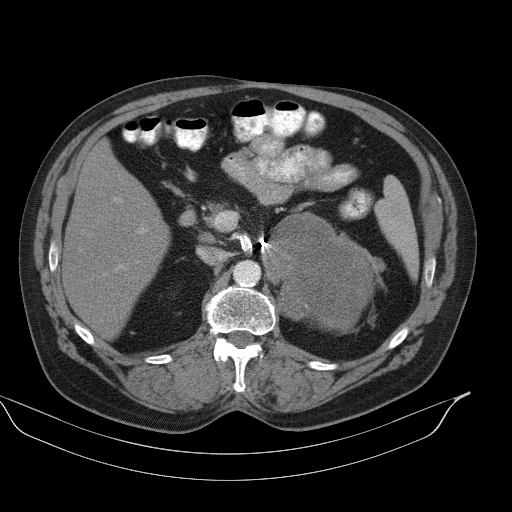
Contrast-enhanced abdominal CT, one axial slice; position 63 of 92 along the scan axis; reconstruction kernel B41s; intravenous contrast given; soft-tissue window (W 400 / L 40 HU); 5 mm slice thickness; 512 × 512 image matrix, field of view 449 × 449 mm. Patient: male, 56 years. From the clinical record (not read from this slice): diagnosis: adrenocortical carcinoma; tumour side: left adrenal; tumour size at pathology: 15 cm; Ki-67 index: 35 %; stage (as recorded): 4.
Structures marked on this image (semi-automatically segmented with operator editing):
- mass: bounding box <272,214,373,330> (left, top, right, bottom; pixels)